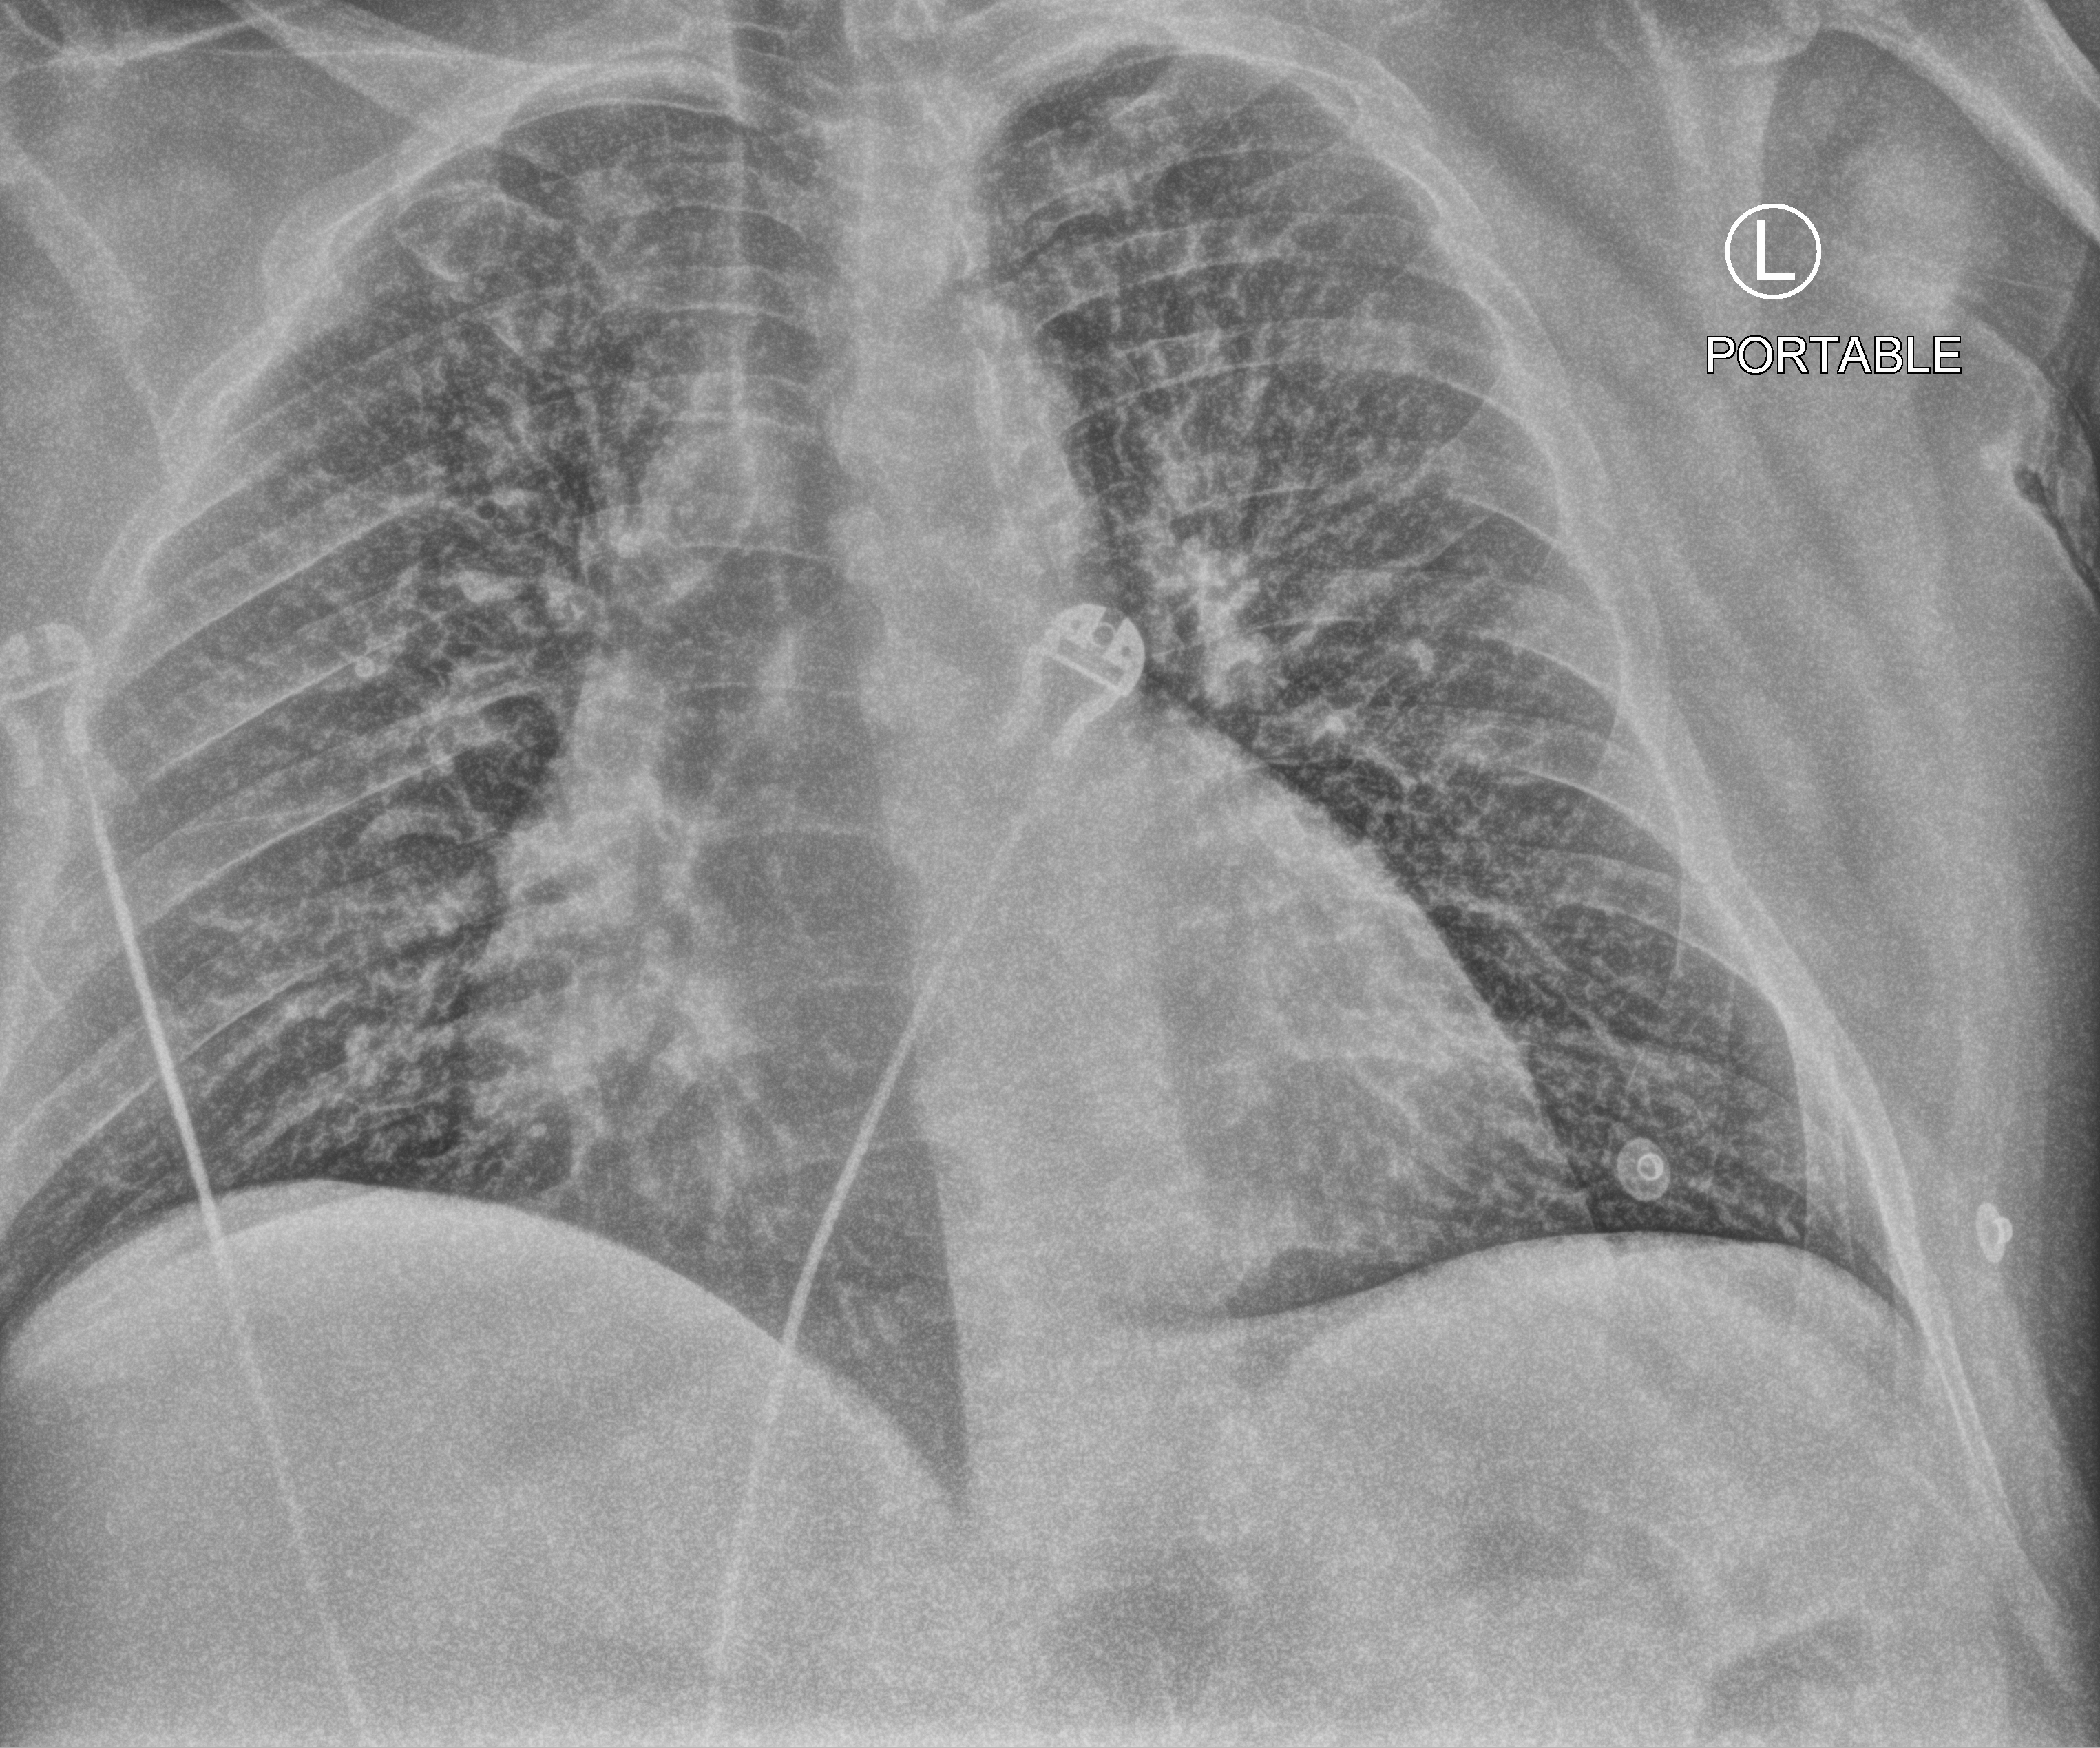
Chest X-ray (portable); anteroposterior (AP) projection. Male patient hospitalised with COVID-19, age 18–59 years.
Hospital-stay facts (about this admission, not read from this image; timing relative to this image not recorded): COPD (admission record): no; admitted to intensive care during this hospital stay: no.